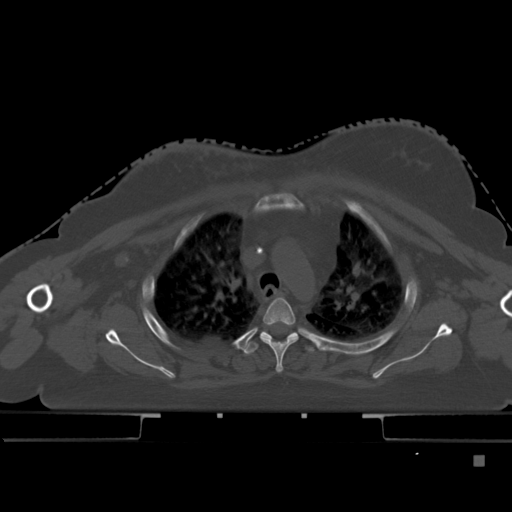
CT including the spine, one axial slice. Bone window (W 1800 / L 400 HU). 1.5 mm slice thickness. 512 × 512 image matrix, field of view 404 × 404 mm. Patient: female, 33 years. From the clinical record (not read from this slice): primary cancer: breast; vertebrae with lytic lesions (as recorded): T1.
Annotated regions visible in this slice (semi-automatic segmentation, software-assisted and operator-edited):
- T3 vertebra: bounding box [x1, y1, x2, y2] px = [260, 297, 299, 373]
- T4 vertebra: [244, 331, 318, 354]